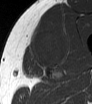
MRI of an extremity soft-tissue mass, one axial slice; slice 40 of 62 in the series (ordered by position); MR volume resampled by the dataset authors to the PET/CT grid (not the native acquisition matrix); 3.27 mm slice thickness; 92 × 104 image matrix, field of view 90 × 102 mm. Male patient. From the clinical record (not read from this slice): histological type: mixoid liposarcoma; grade: low; site of the primary tumour: left thigh.
Structures marked on this image (expert contour drawn on MRI and transferred to this co-registered scan by the dataset authors):
- gross tumour volume (mass): bounding box (x1, y1, x2, y2) in pixels: (28, 28, 68, 68)